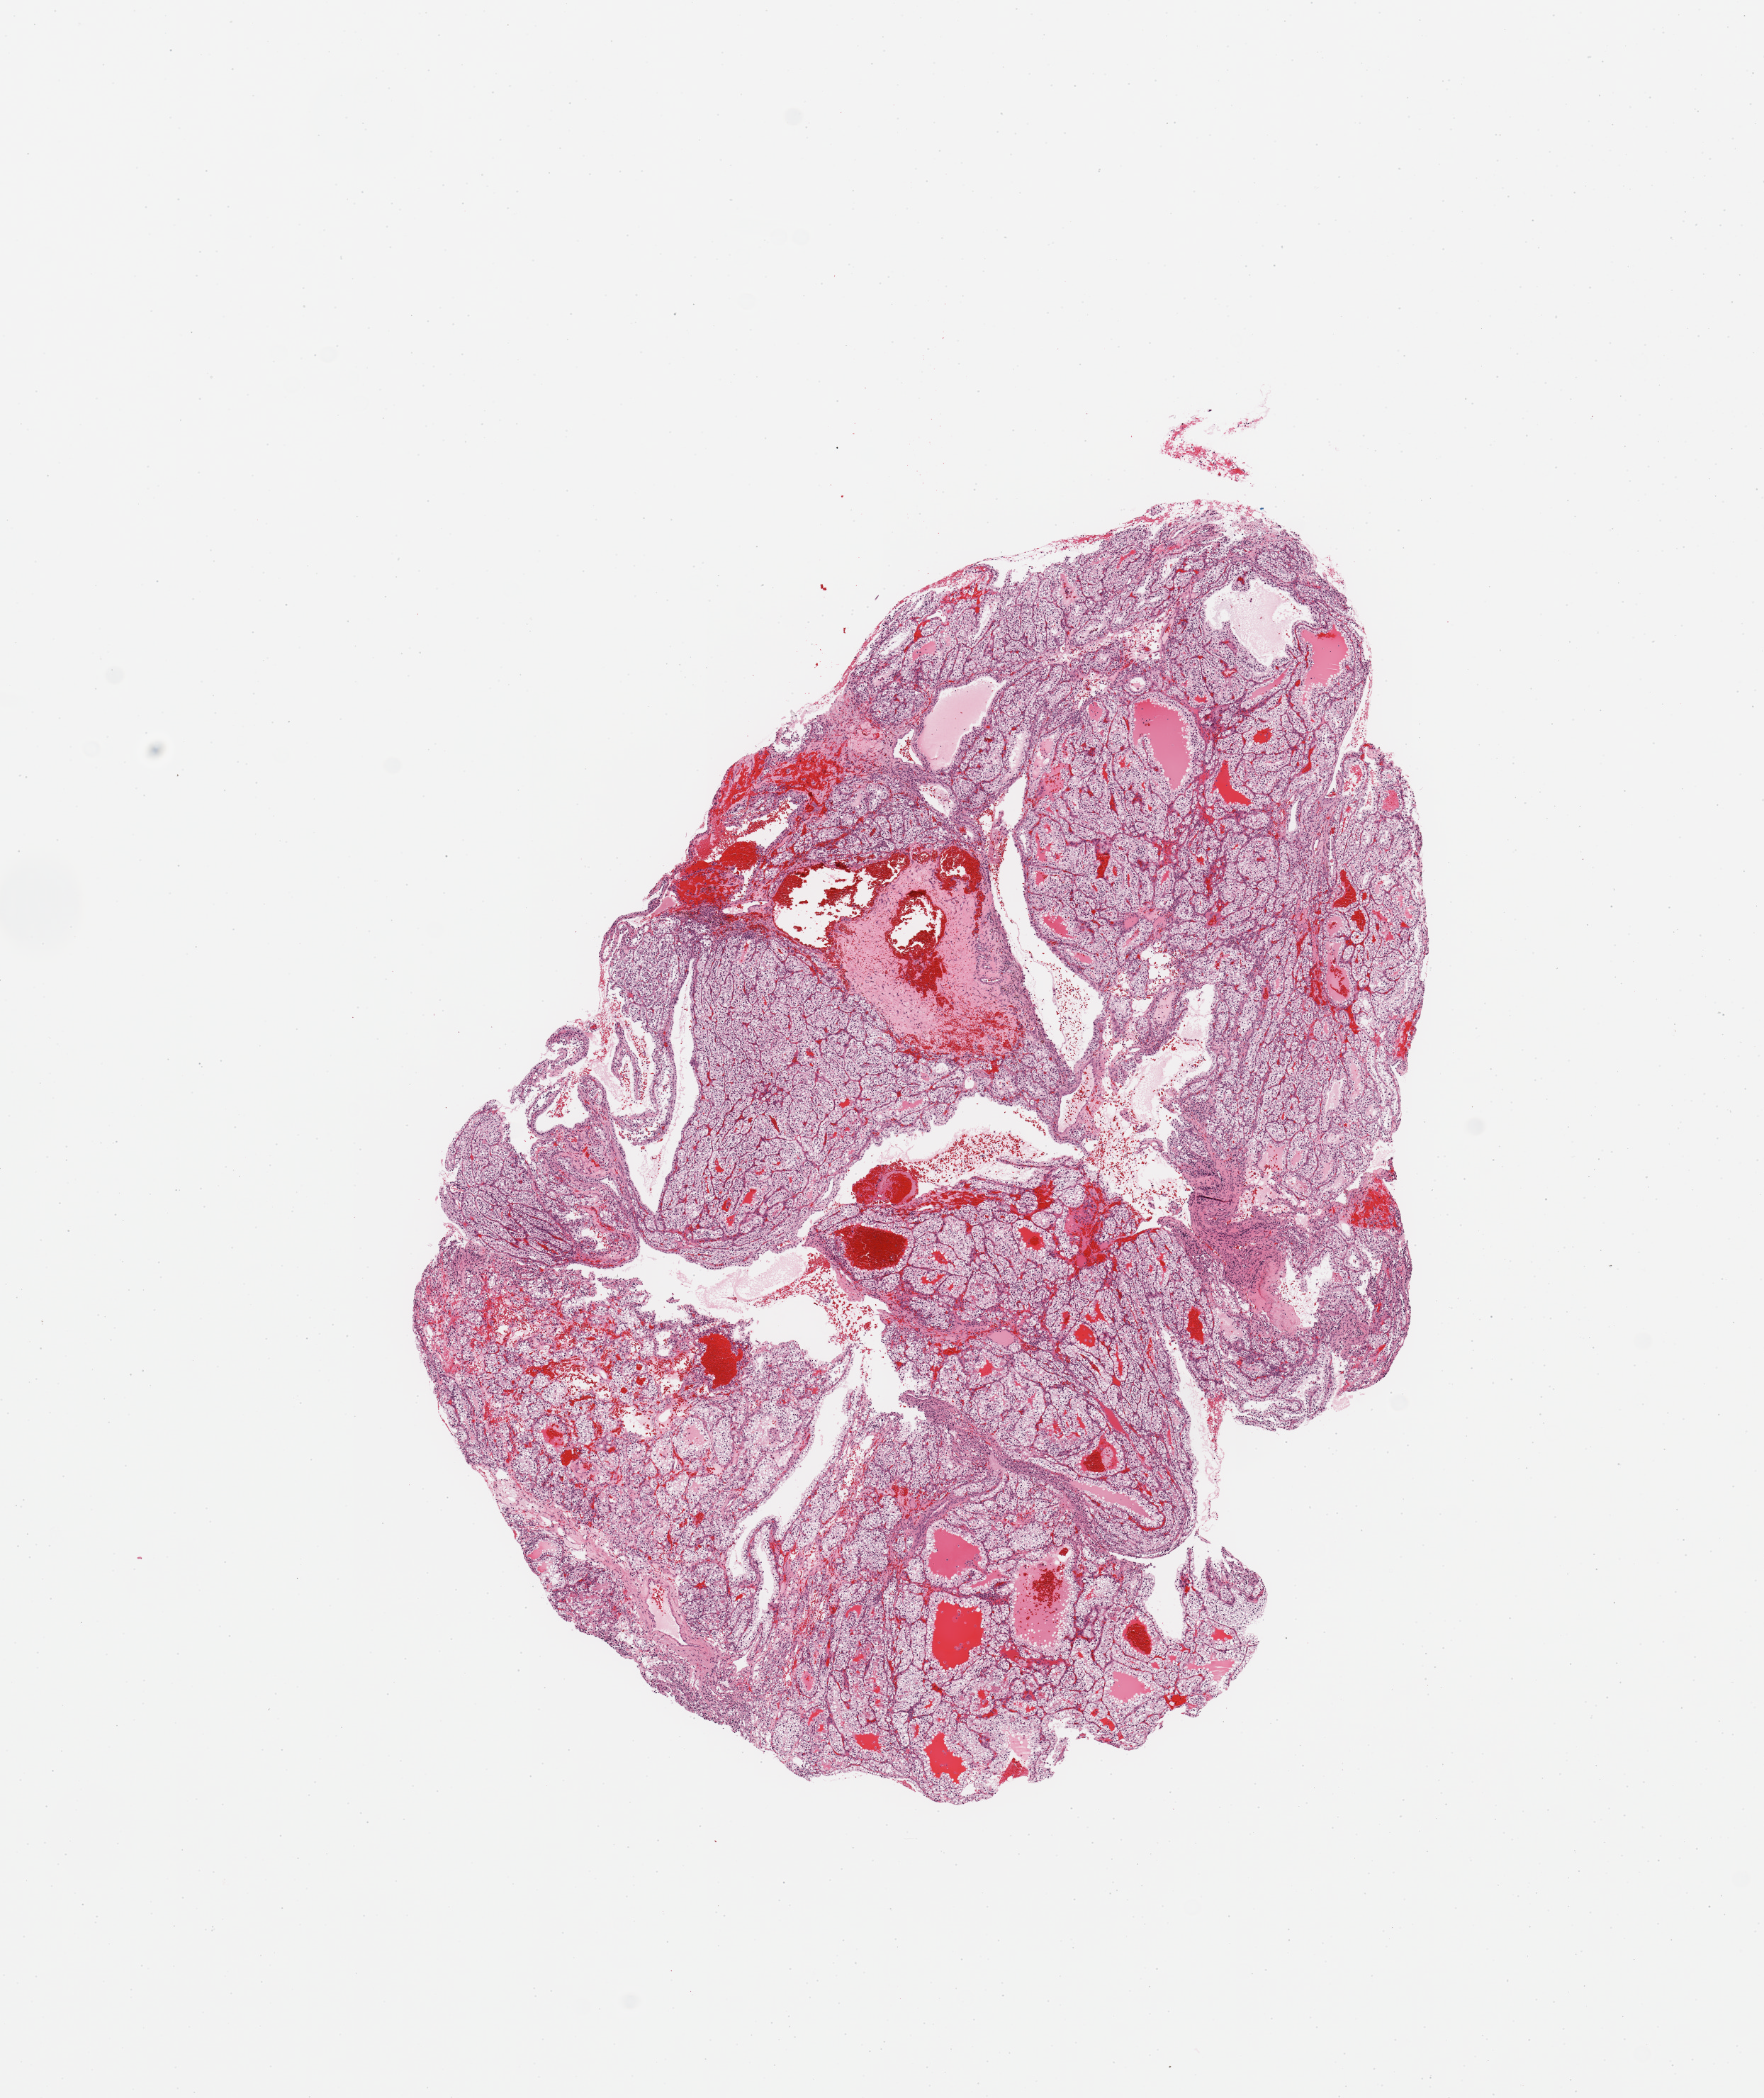
Whole-slide histology image, H&E, shown as a low-resolution overview of the whole scanned area (about 9.8 x 11.7 mm, from a 20x scan). Tumour tissue sample, sampled site: kidney. Patient: male, age 63 years. Histologic grade: G2 (moderately differentiated). Pathologist review of this section (percent, as recorded): tumour nuclei 90%, necrosis 0%.
AJCC pathologic stage: I. Diagnosis: Renal cell carcinoma, NOS.